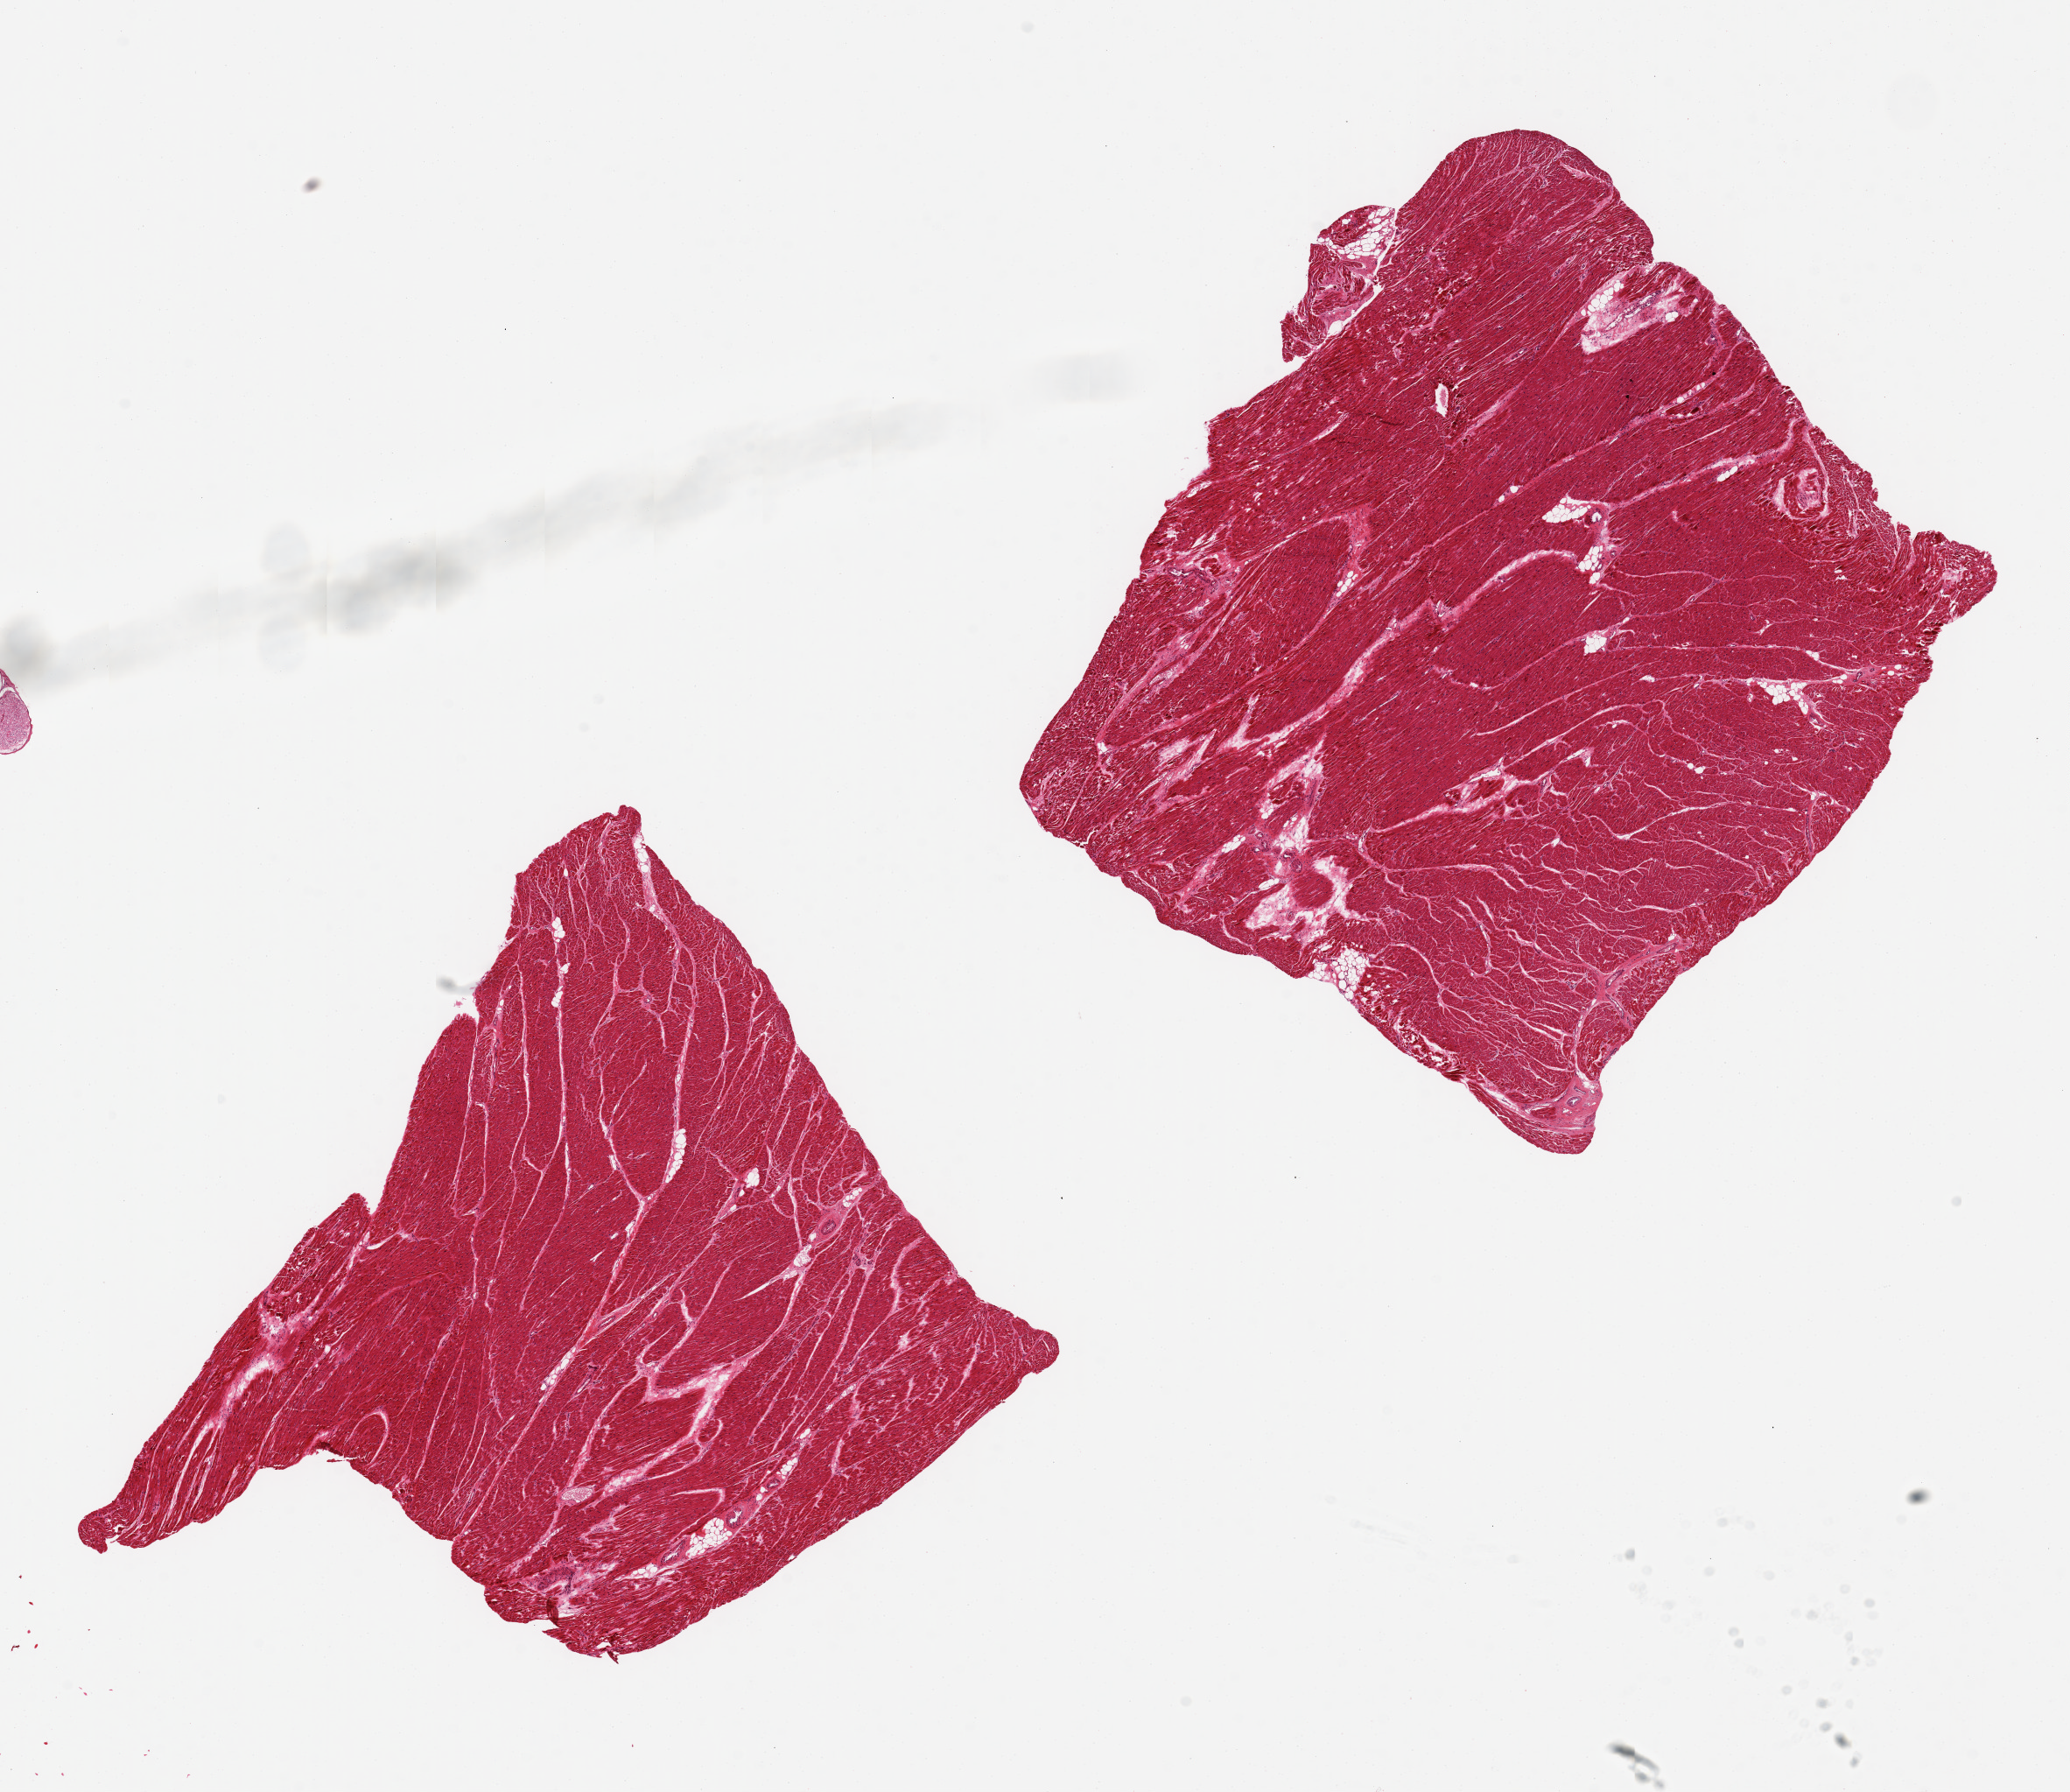
Whole-slide image, H&E stain — low-resolution overview of the scanned area, about 18.7 x 16.2 mm (acquisition: 20x scan), PAXgene-fixed paraffin-embedded (PFPE) section, section of heart (target tissue), tissue donor sample. Donor: male.
Review note (as recorded): 2 pieces 7x6mm. No significant ischemic changes.